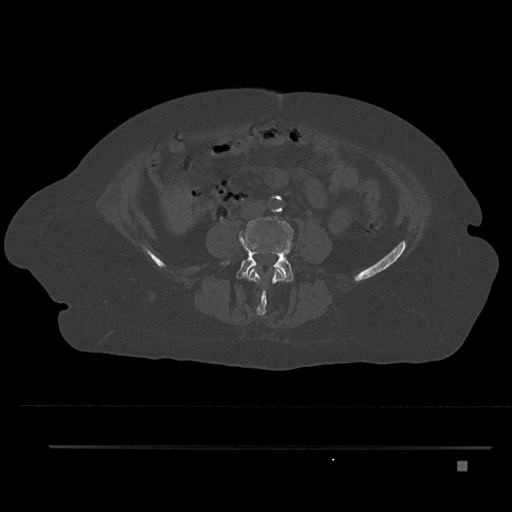
CT including the spine, one axial slice; position 96 of 797 along the scan axis; reconstruction kernel Br40s/3; bone window (W 1800 / L 400 HU); 0.5 mm slice thickness; 512 × 512 image matrix, field of view 437 × 437 mm. Female patient, age 76 years. From the clinical record (not read from this slice): primary cancer: lung.
Annotated regions visible in this slice (semi-automatically segmented with operator editing):
- L3 vertebra: box from (x=248, y=267) to (x=285, y=315) px
- L4 vertebra: (x=222, y=216)–(x=294, y=283)